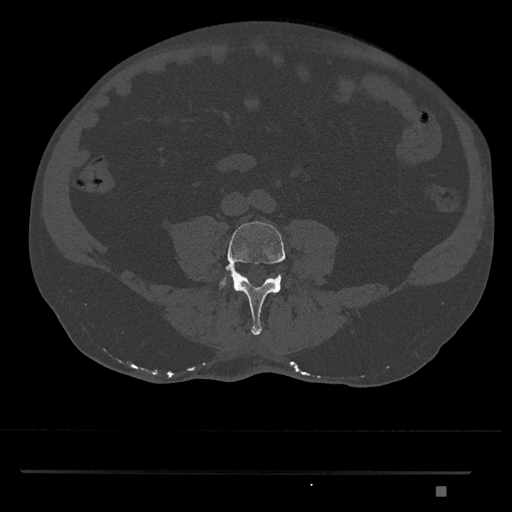
CT including the spine, one axial slice. Slice 611 of 1134 in the series (ordered by position). Reconstruction kernel Br40s/3. 120 kVp. Bone window (W 1800 / L 400 HU). 512 × 512 image matrix, field of view 429 × 429 mm. Male patient, age 65 years. Case-level facts recorded for this patient, not image findings: primary cancer: prostate.
Outlined on this slice (semi-automatic segmentation, software-assisted and operator-edited):
- L4 vertebra: bounding box <219,221,286,335> (left, top, right, bottom; pixels)